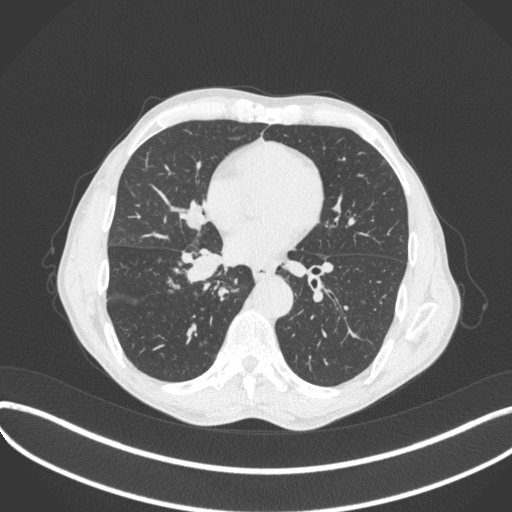
Chest CT, one axial slice; reconstruction kernel B31f; lung window (W 1500 / L -600 HU); 512 × 512 image matrix, field of view 400 × 400 mm. Patient: male, 65 years. Case-level facts recorded for this patient, not image findings: clinical TNM (as recorded): T2a N0 M0; histopathological grade: G2.
Outlined on this slice (bounding box drawn by a radiologist):
- lung tumour (recorded histology: squamous cell carcinoma): bounding box [x1, y1, x2, y2] px = [180, 245, 233, 282]